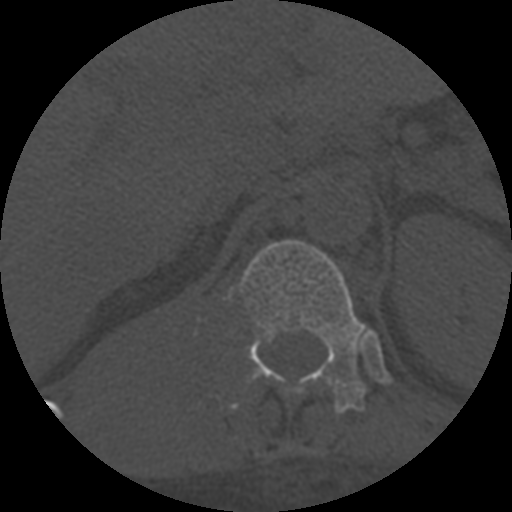
CT including the spine, one axial slice; slice 317 of 708 in the series (ordered by position); reconstruction kernel STANDARD; one of 3 acquisitions stored at this slice position; bone window (W 1800 / L 400 HU); 1.25 mm slice thickness; 512 × 512 image matrix, field of view 160 × 160 mm. Patient age 55 years. Case-level facts recorded for this patient, not image findings: primary cancer: colon; vertebrae with lytic lesions (as recorded): T12, L1, L5.
Annotated regions visible in this slice (semi-automatically segmented with operator editing):
- T11 vertebra: box from (x=233, y=406) to (x=236, y=408) px
- T12 vertebra: (x=228, y=240)–(x=368, y=414)